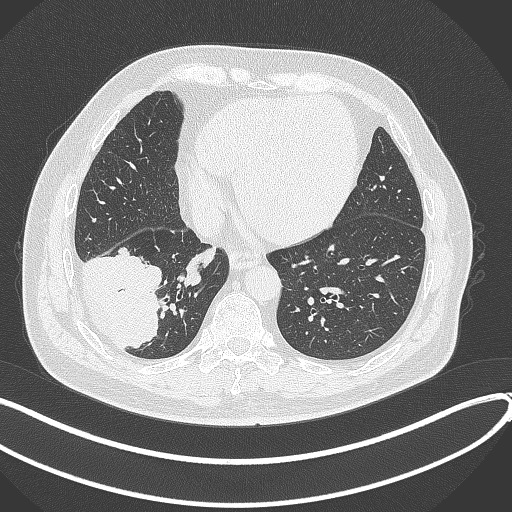
Chest CT, one axial slice; position 111 of 360 along the scan axis; 120 kVp; lung window (W 1500 / L -600 HU); 1 mm slice thickness; 512 × 512 image matrix, field of view 400 × 400 mm. Male patient, age 59 years.
Outlined on this slice (bounding box drawn by a radiologist):
- lung tumour (recorded histology: adenocarcinoma): bounding box [x1, y1, x2, y2] px = [80, 245, 163, 352]